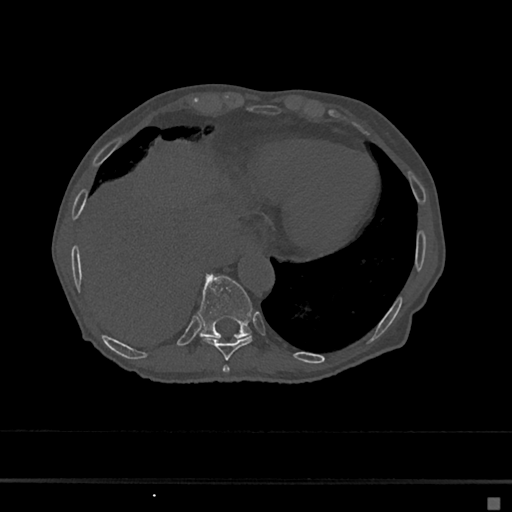
CT including the spine, one axial slice. Position 250 of 797 along the scan axis. Reconstruction kernel Br40s/3. 120 kVp. Bone window (W 1800 / L 400 HU). 0.5 mm slice thickness. 512 × 512 image matrix. Female patient, age 68 years. From the clinical record (not read from this slice): primary cancer: renal.
Outlined on this slice (semi-automatically segmented with operator editing):
- T10 vertebra: box from (x=197, y=275) to (x=253, y=339) px
- T8 vertebra: (x=223, y=365)–(x=230, y=373)
- T9 vertebra: (x=202, y=336)–(x=253, y=361)